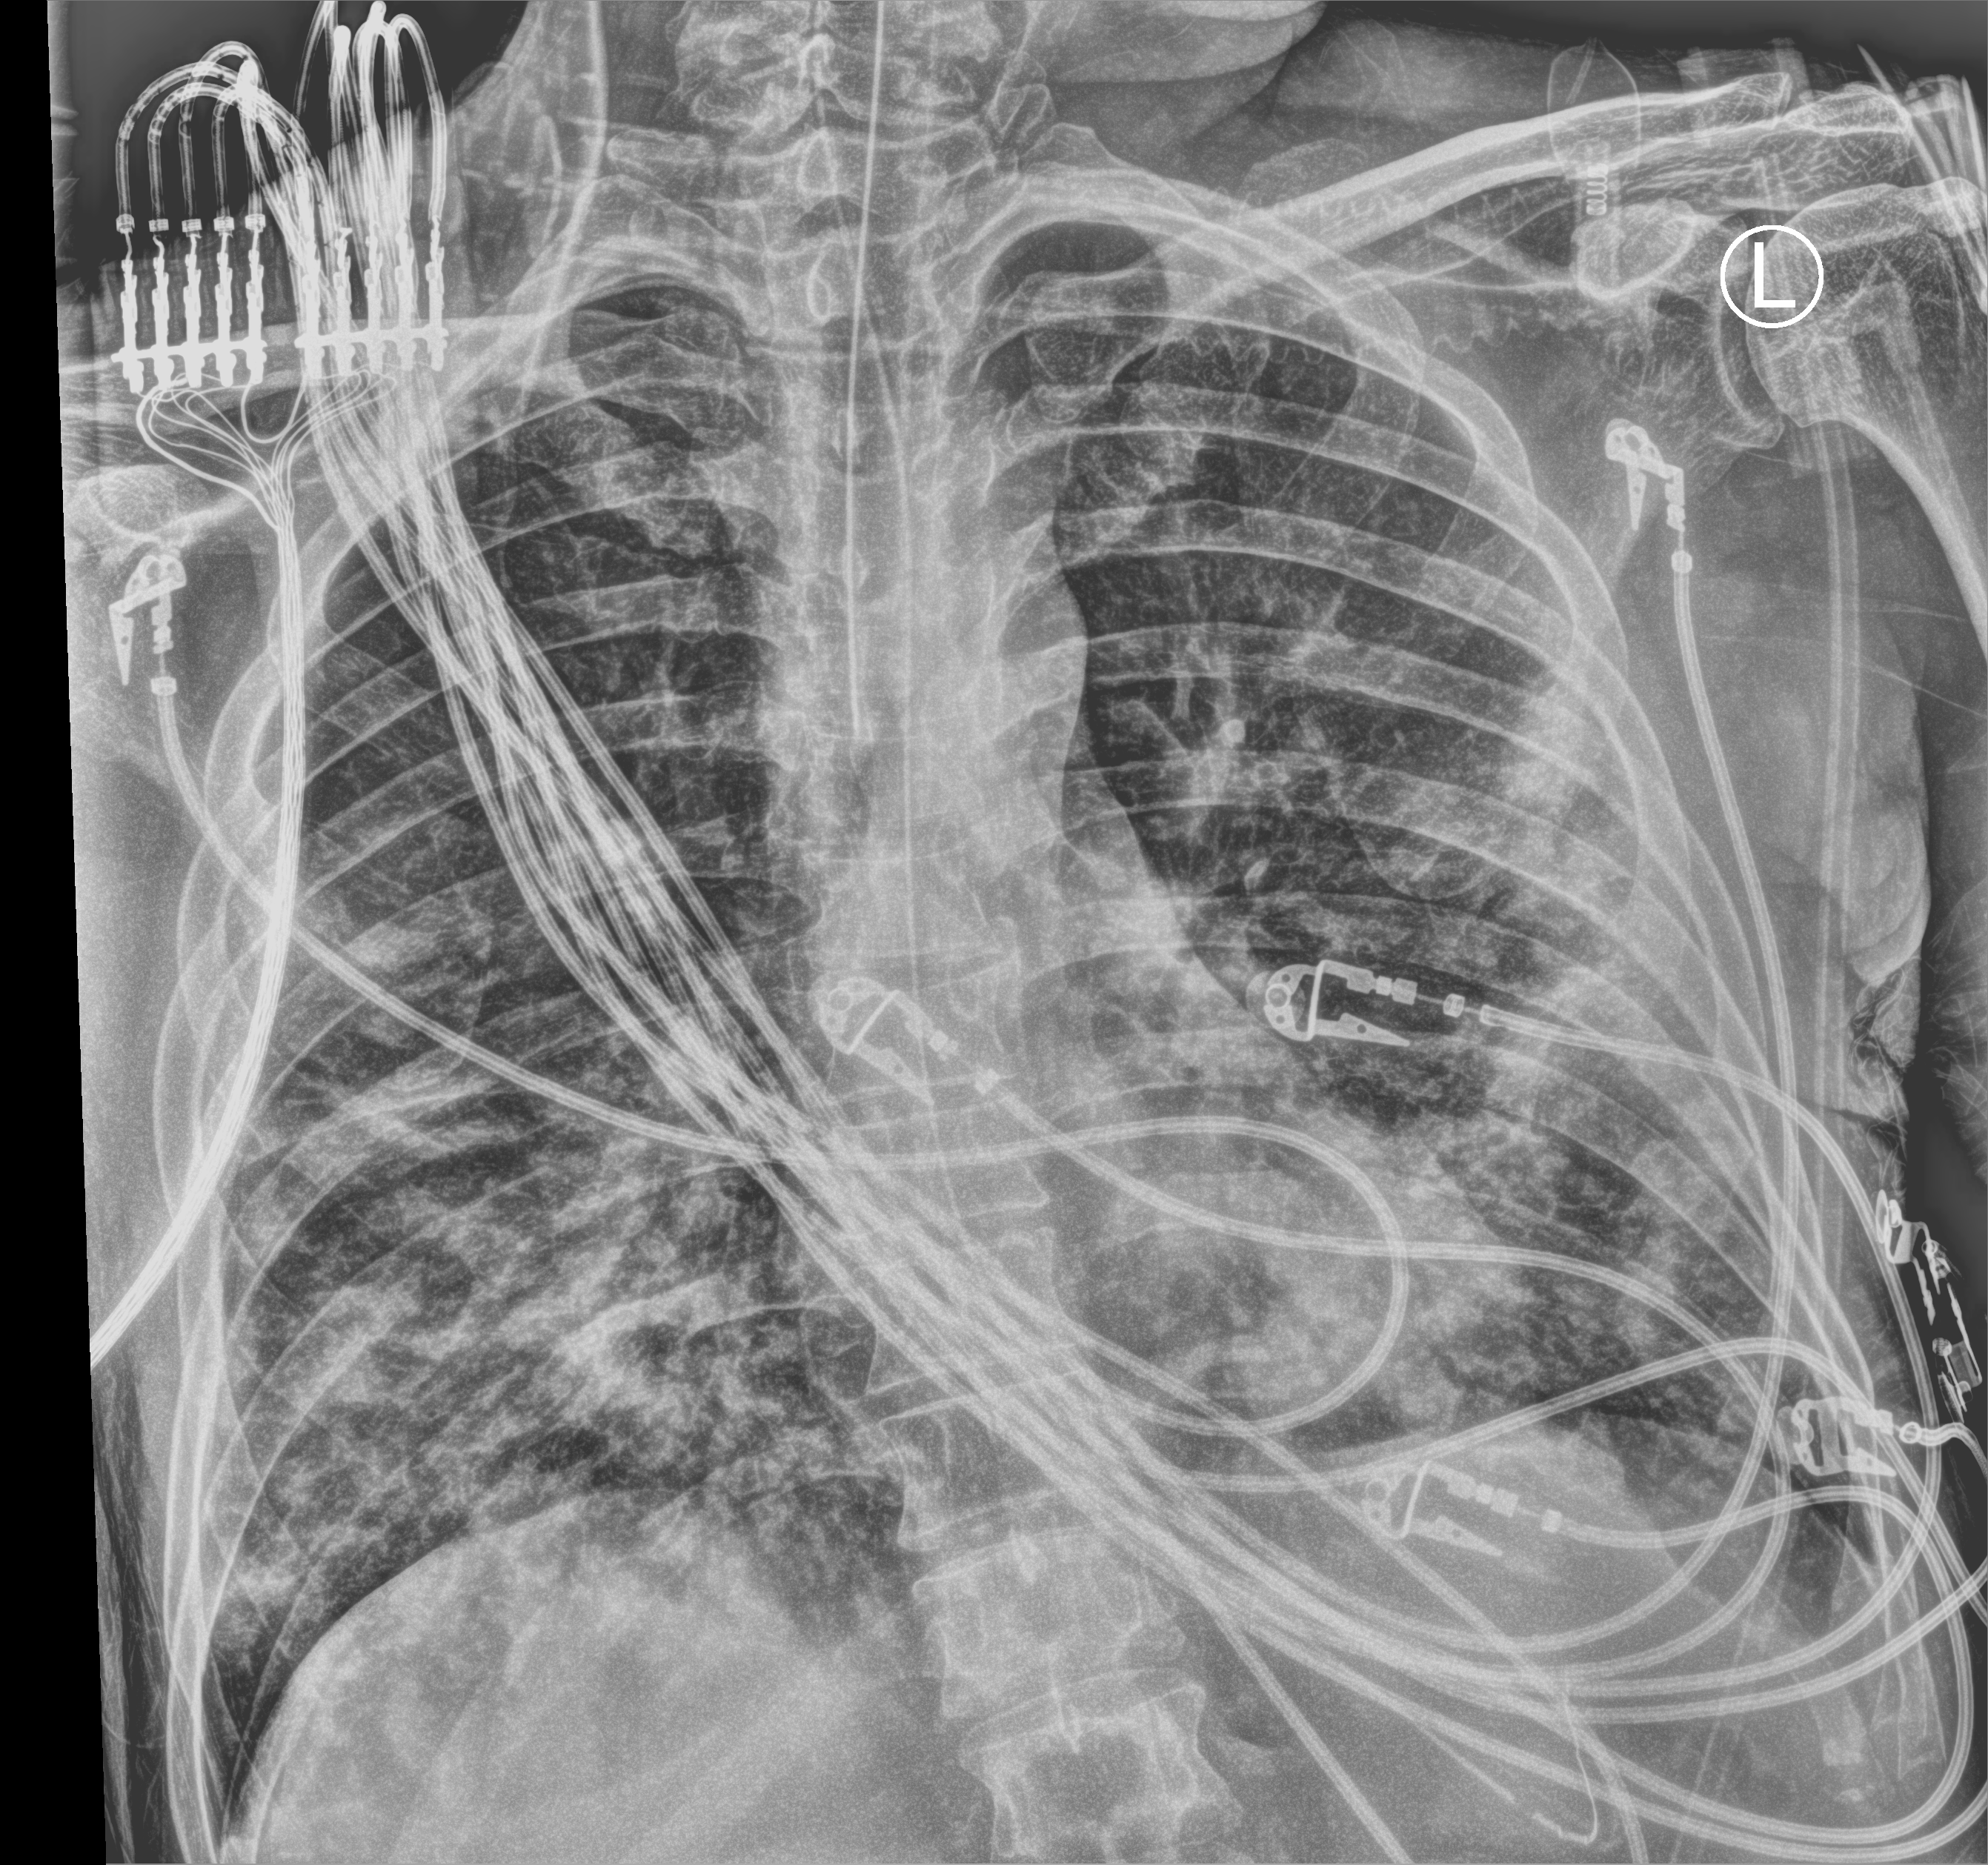
Chest X-ray (portable); anteroposterior (AP) projection. Male patient hospitalised with COVID-19, age 18–59 years.
Admission-level facts for this patient (not findings on this image; timing relative to this image not recorded):
- diabetes (admission record): yes